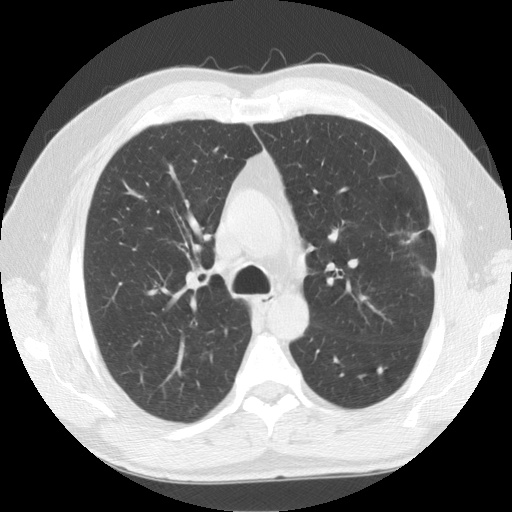
Low-dose screening chest CT, one axial slice; position 98 of 141 along the scan axis; lung window (W 1500 / L -600 HU); 2.5 mm slice thickness; 512 × 512 image matrix.
Outlined on this slice (expert manual segmentation):
- lesion 1 (tumor, upper lobe of left lung): bounding box <406,231,421,243> (left, top, right, bottom; pixels)